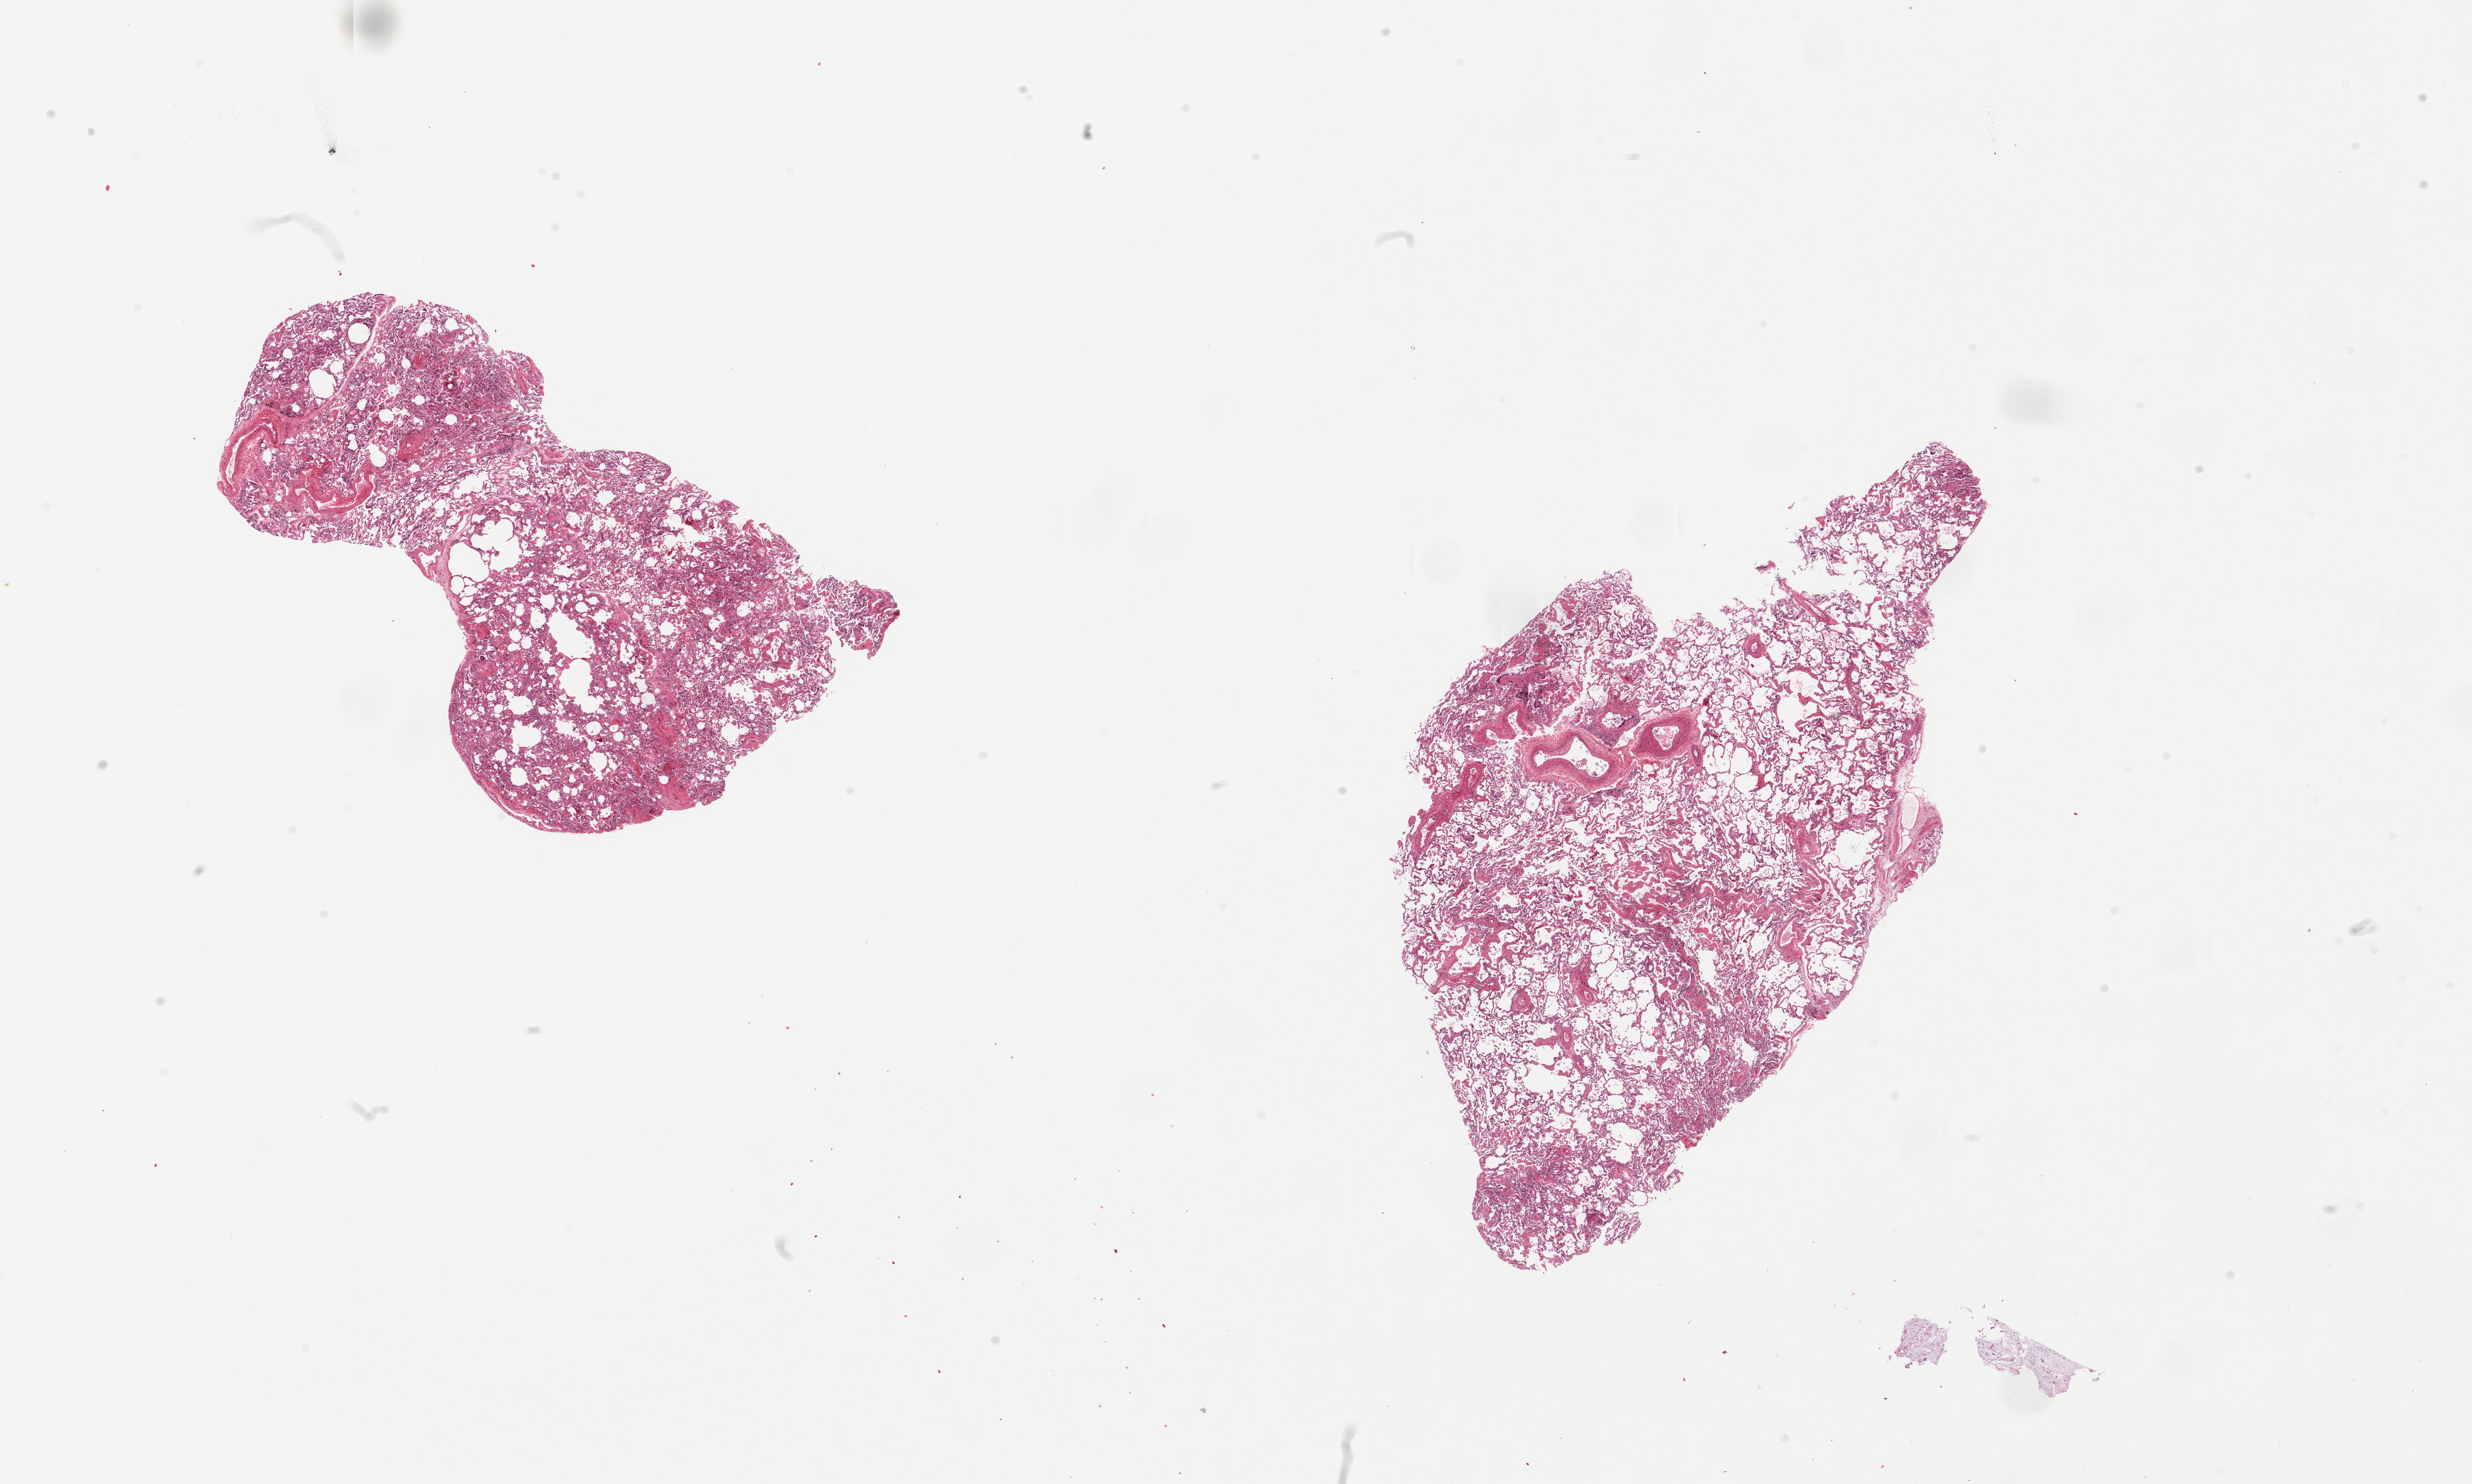
Hematoxylin and eosin (H&E) whole-slide image — a low-resolution overview of the entire scanned area, about 27.6 x 16.5 mm, PAXgene-fixed, paraffin-embedded tissue, target tissue: lung, donor tissue sample. Female donor.
Reviewer comment on this tissue sample: 2 pieces, hemosiderin-laden macrophages, focal emphysematous change and fibrosis.